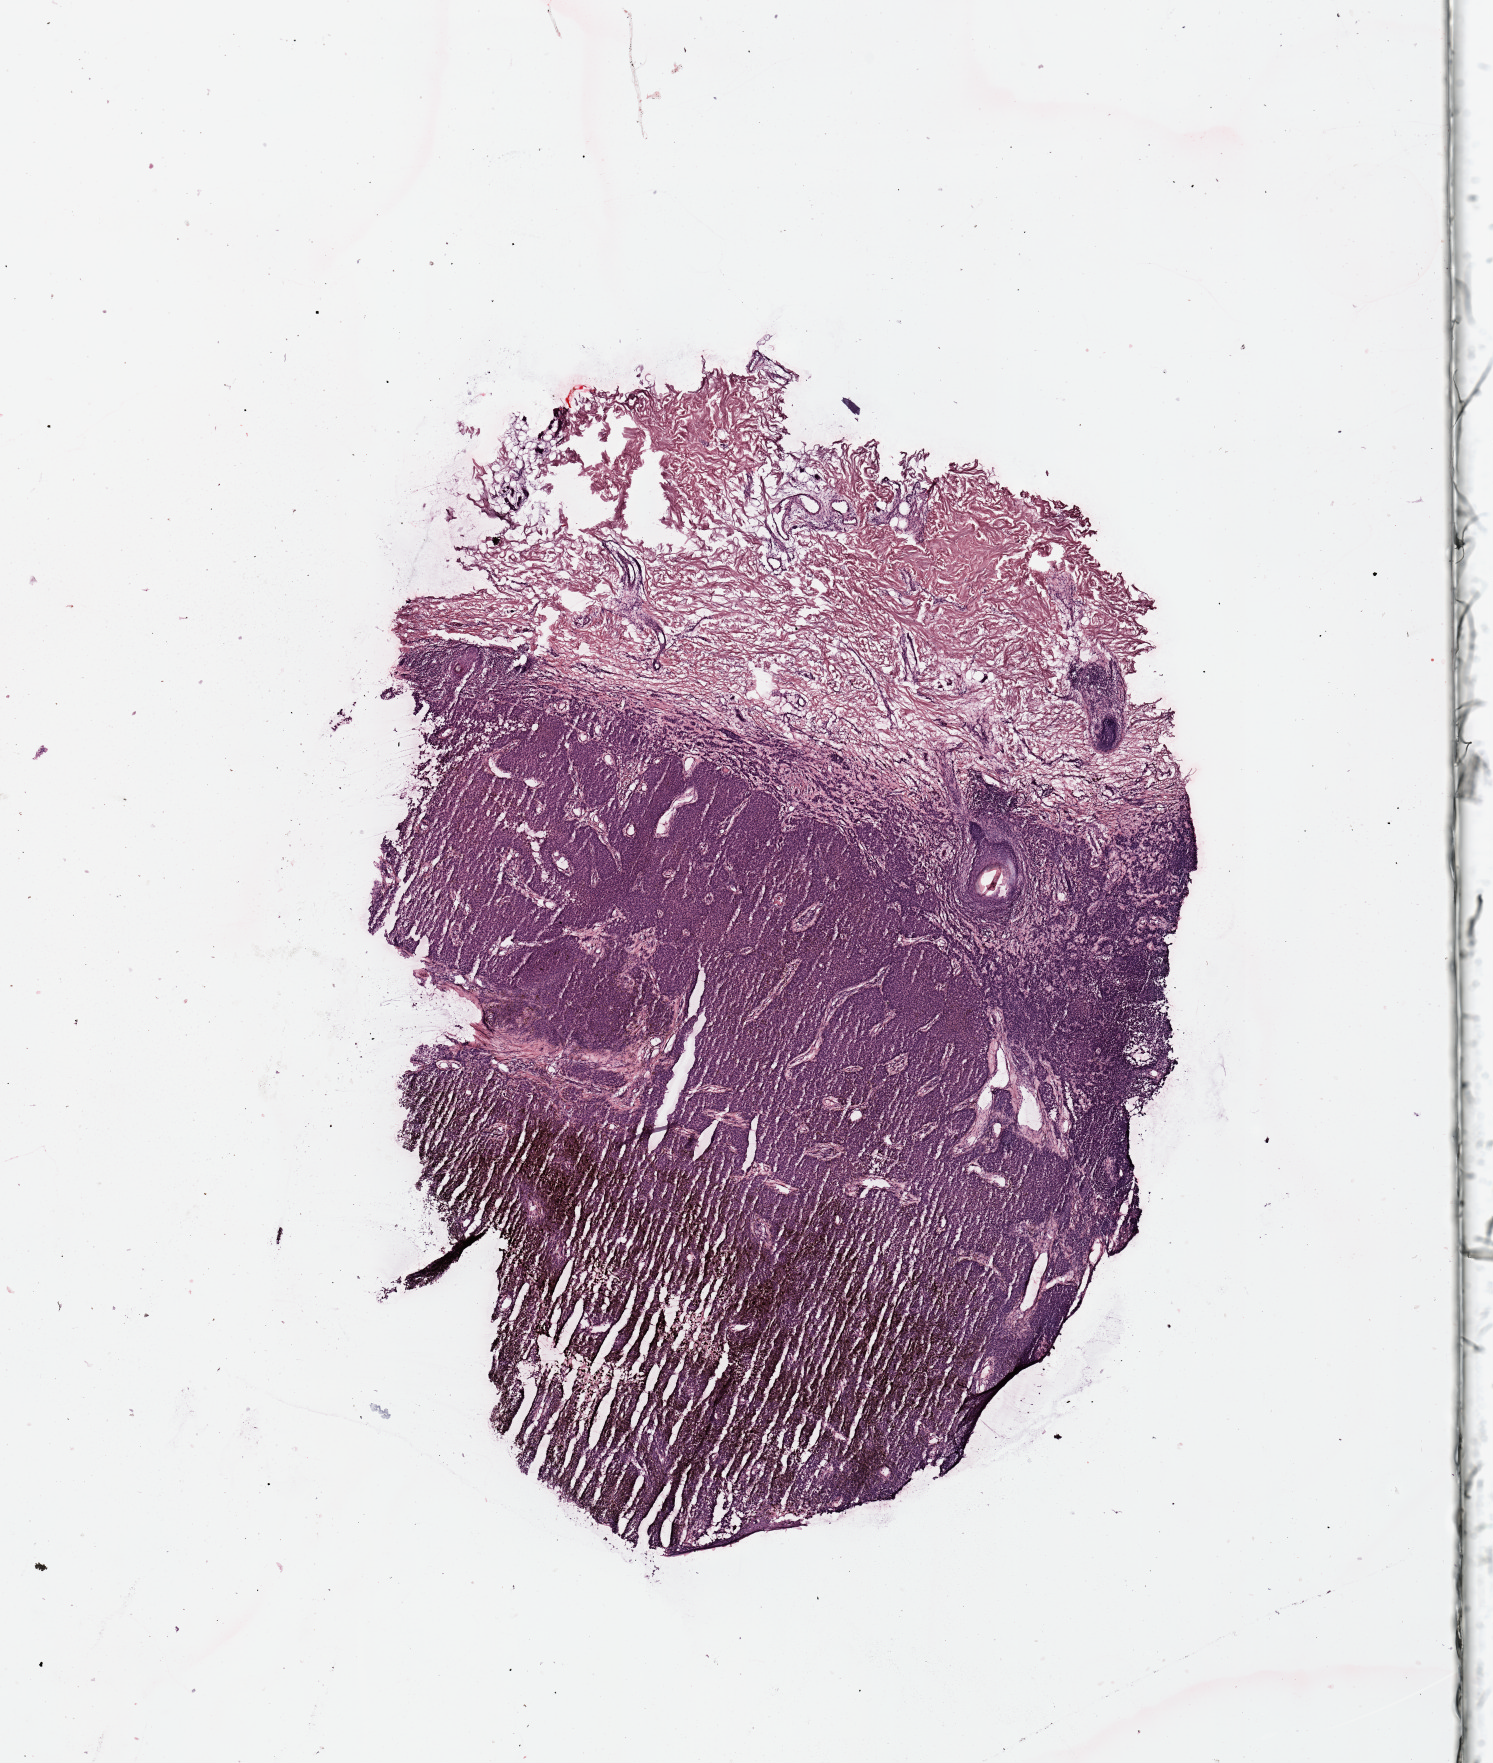
Whole-slide histology image, H&E, a low-resolution overview of the entire scanned area, about 11.8 x 13.9 mm. Melanoma tumour tissue; sampled site not recorded. 53-year-old female patient.
Patient diagnosis (cohort enrolment): cutaneous melanoma (skin).